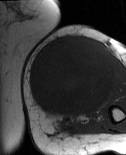
MRI of an extremity soft-tissue mass, one axial slice; slice 30 of 86 in the series (ordered by position); MR volume resampled by the dataset authors to the PET/CT grid (not the native acquisition matrix); 126 × 155 image matrix, field of view 123 × 151 mm. Female patient. From the clinical record (not read from this slice): histological type: pleiomorphic leiomyosarcoma; grade: high; site of the primary tumour: left biceps.
Structures marked on this image (expert contour drawn on MRI and transferred to this co-registered scan by the dataset authors):
- gross tumour volume including surrounding oedema: bounding box (x1, y1, x2, y2) in pixels: (29, 37, 117, 119)
- gross tumour volume (mass): (29, 37, 117, 116)